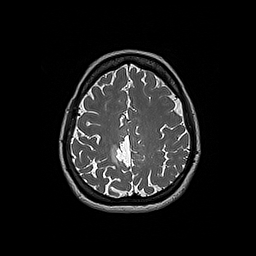
Brain MRI from a brain-tumour surgery series, one axial slice. Position 60 of 192 along the scan axis. 1 mm slice thickness. 256 × 256 image matrix. From the clinical record (not read from this slice): histopathology: Oligodendroglioma; WHO grade: 2; IDH mutation: yes.
Structures marked on this image (outlined manually by an expert reader):
- tumour: bounding box [x1, y1, x2, y2] px = [110, 145, 119, 165]